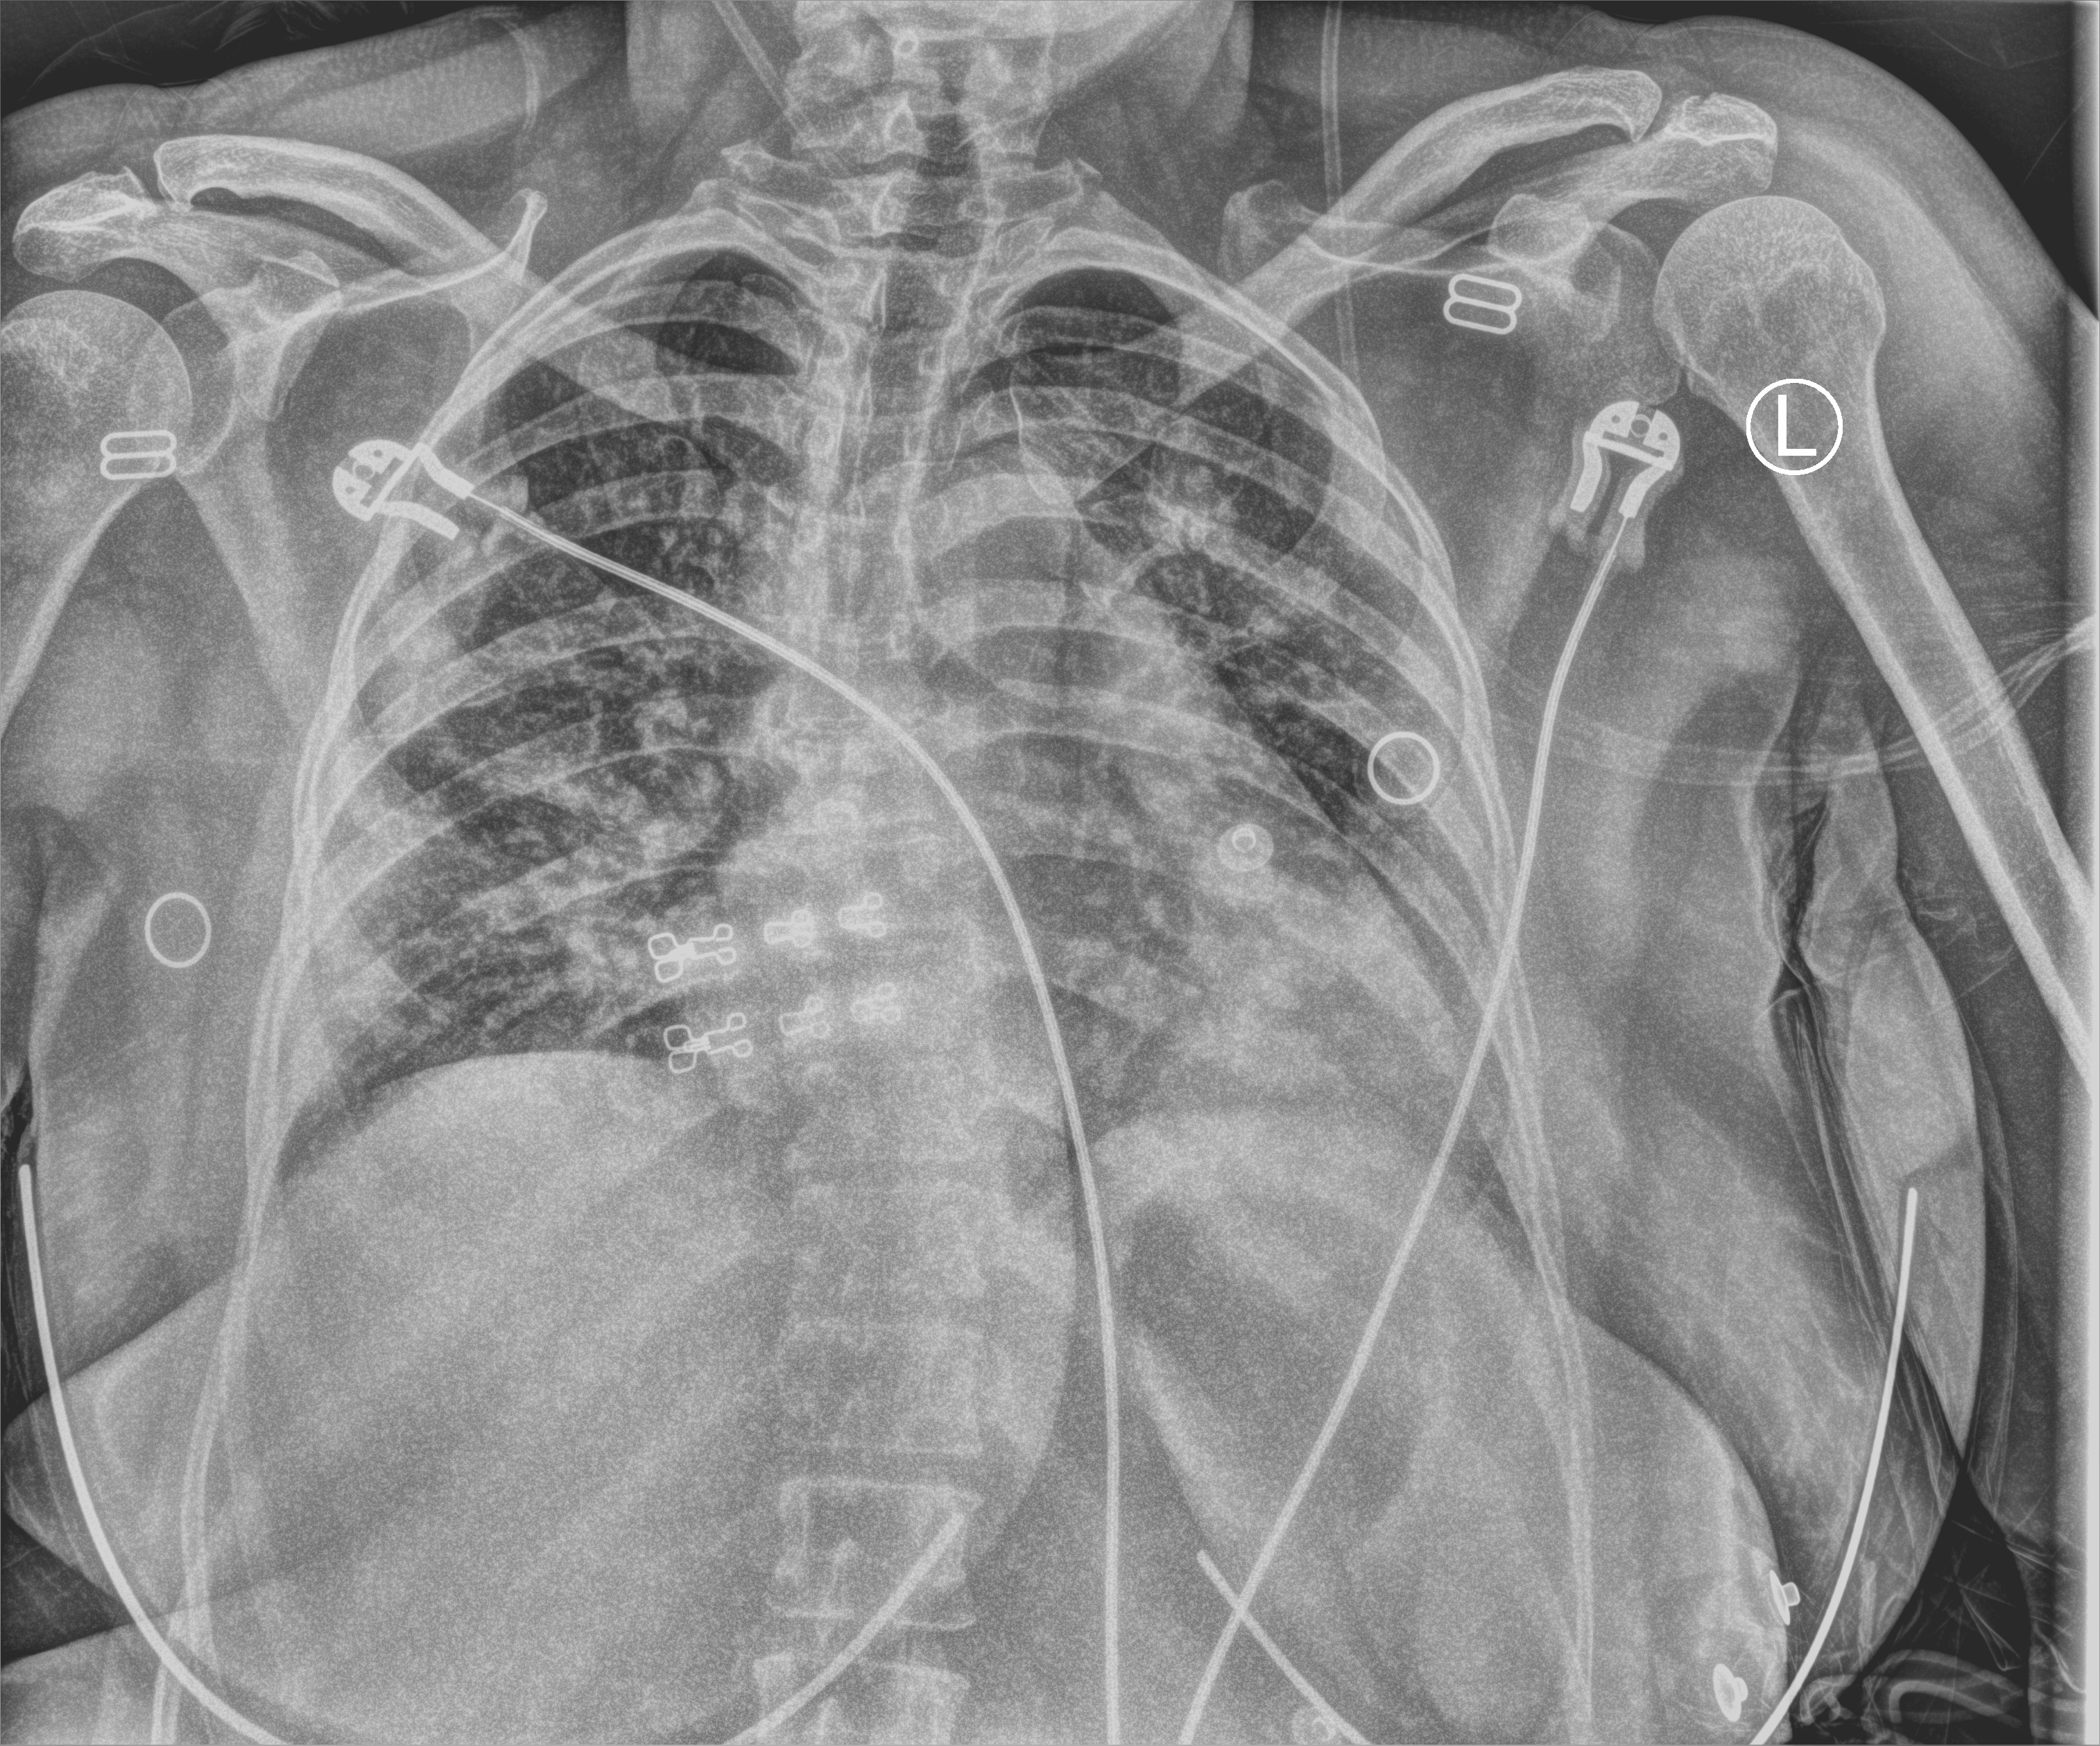
Chest X-ray (portable), anteroposterior (AP) projection. Female patient hospitalised with COVID-19, age 18–59 years.
From the hospital-stay record, not from the radiograph (when in the stay this image was taken is not recorded):
- length of hospital stay: 14 days